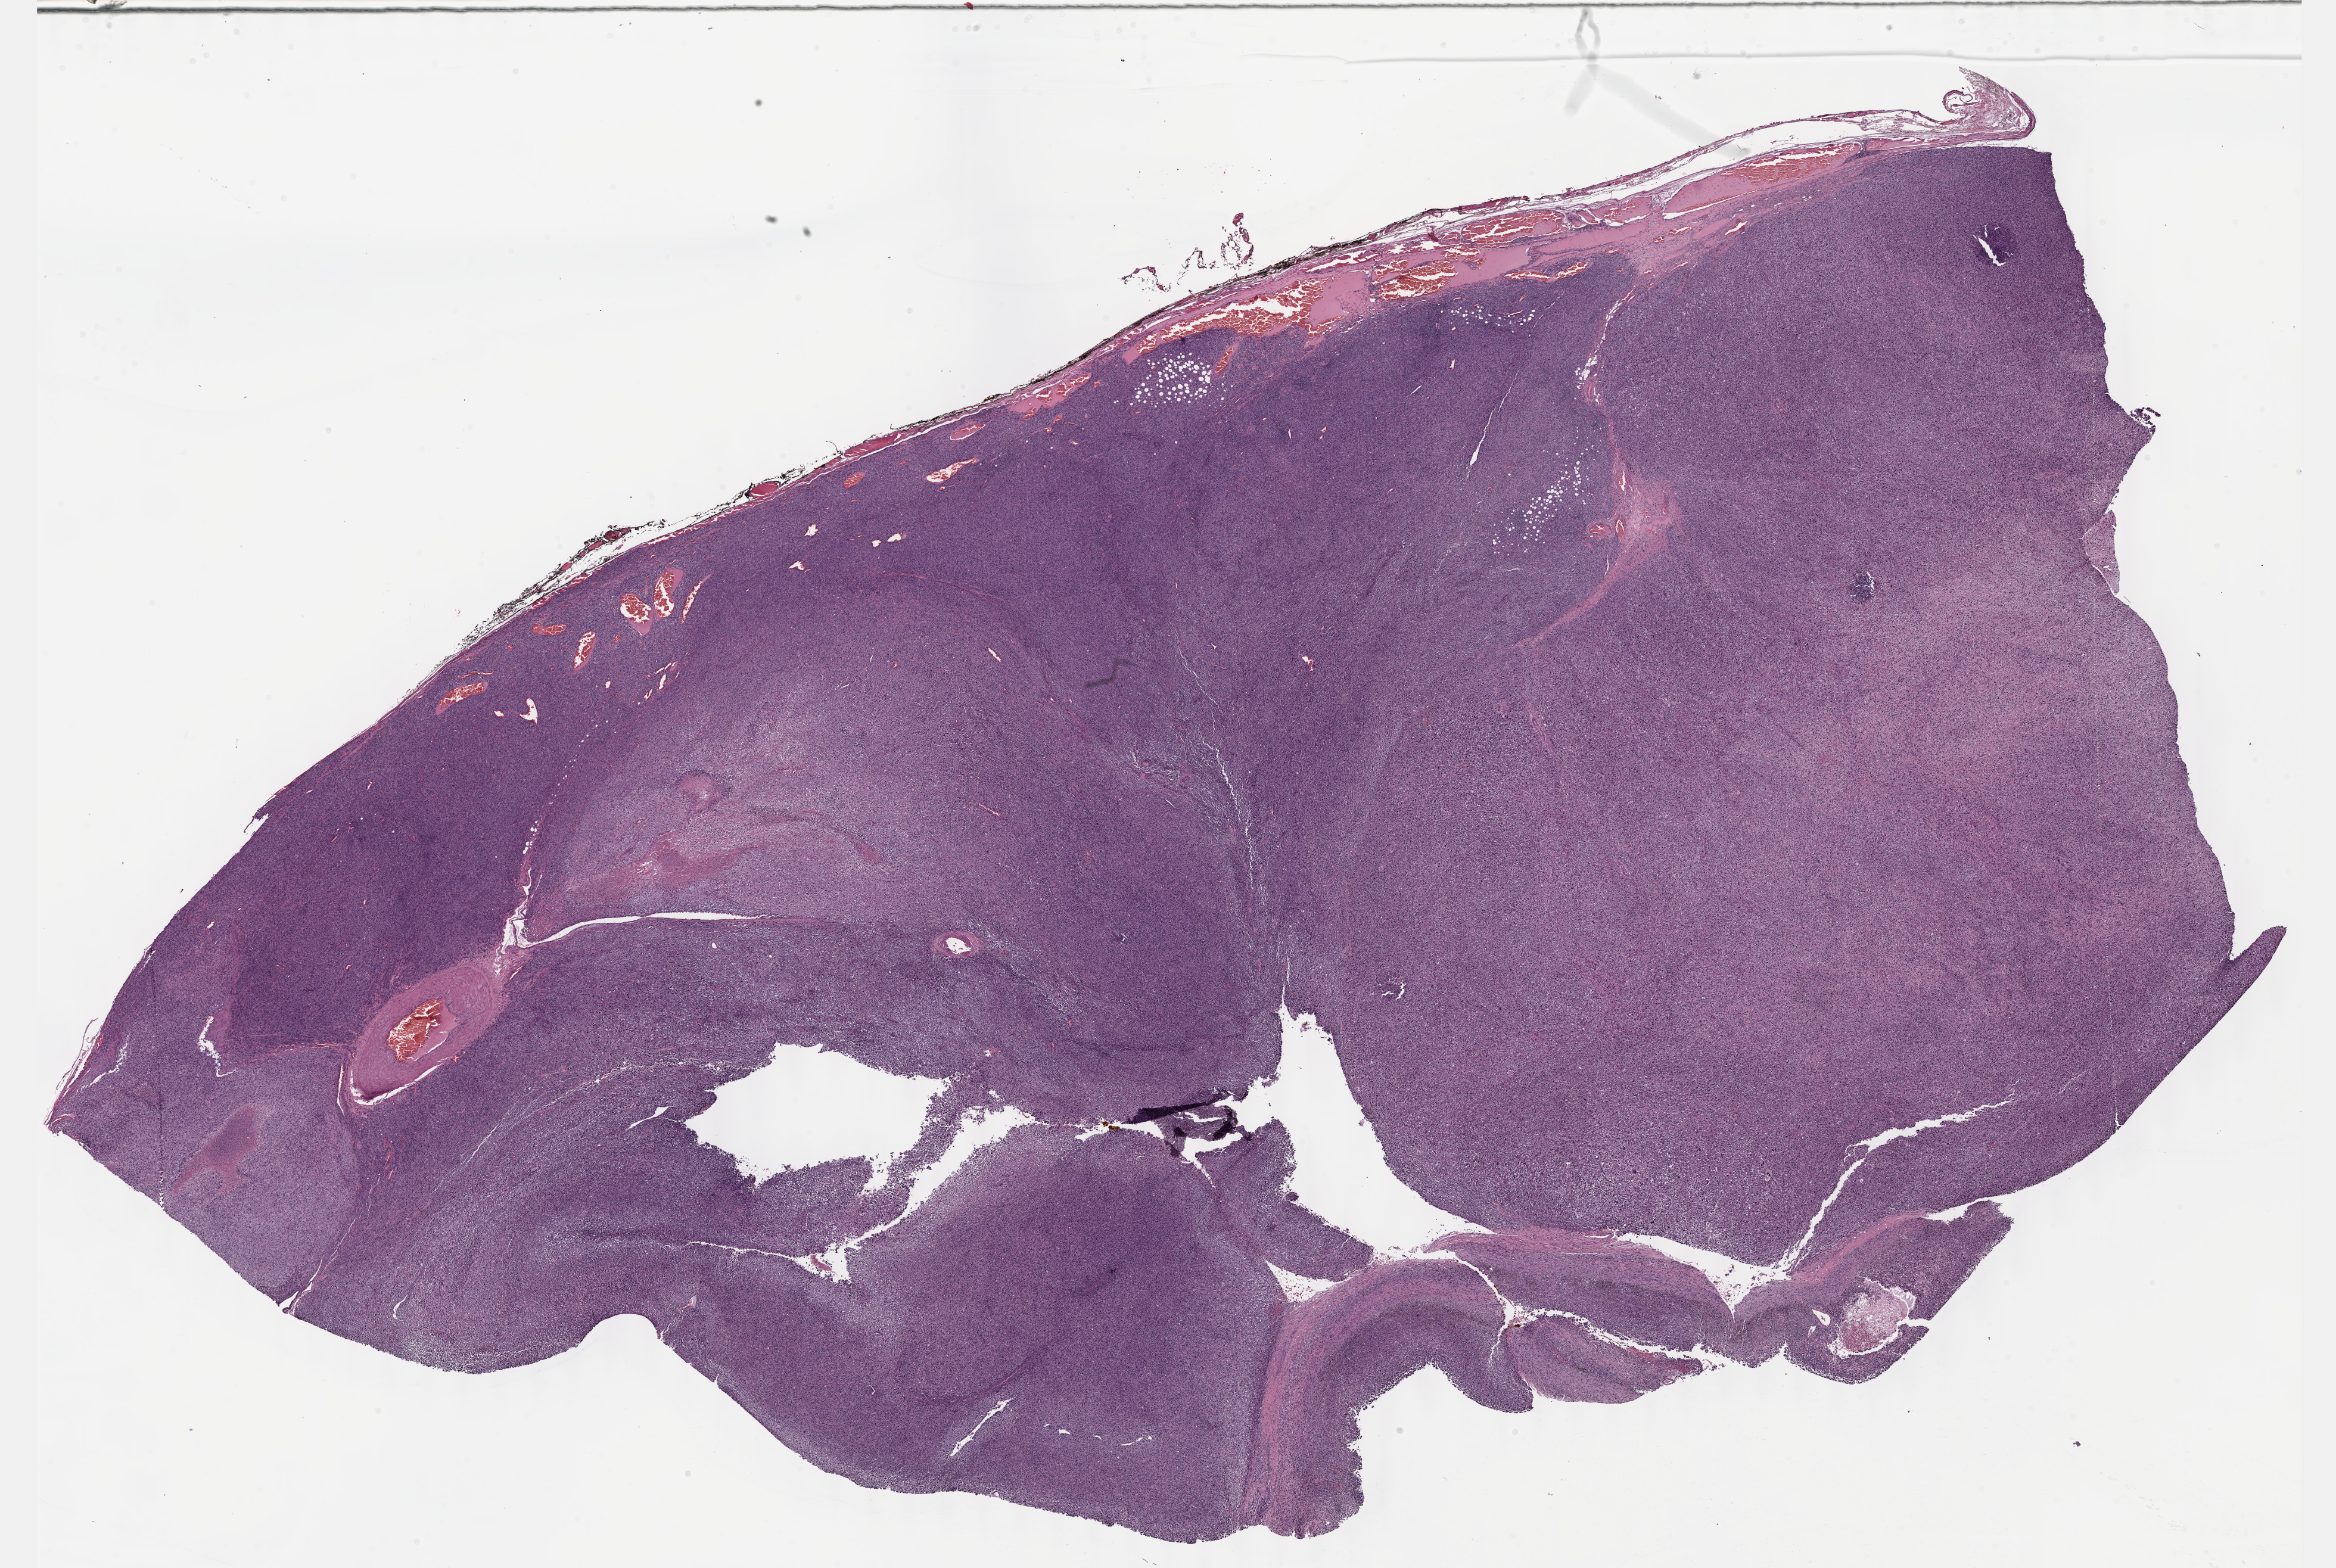
Digitized Hematoxylin and eosin (H&E) stained tissue section (whole slide) — shown as a low-resolution overview of the whole scanned area (about 31.7 x 21.3 mm, acquisition: 40x scan). Formalin-fixed paraffin-embedded (FFPE) diagnostic section. Sample: primary tumour, connective, subcutaneous and other soft tissues. Male, age 29 years at initial diagnosis.
Diagnosis: Malignant peripheral nerve sheath tumor (connective, subcutaneous and other soft tissues of lower limb and hip).